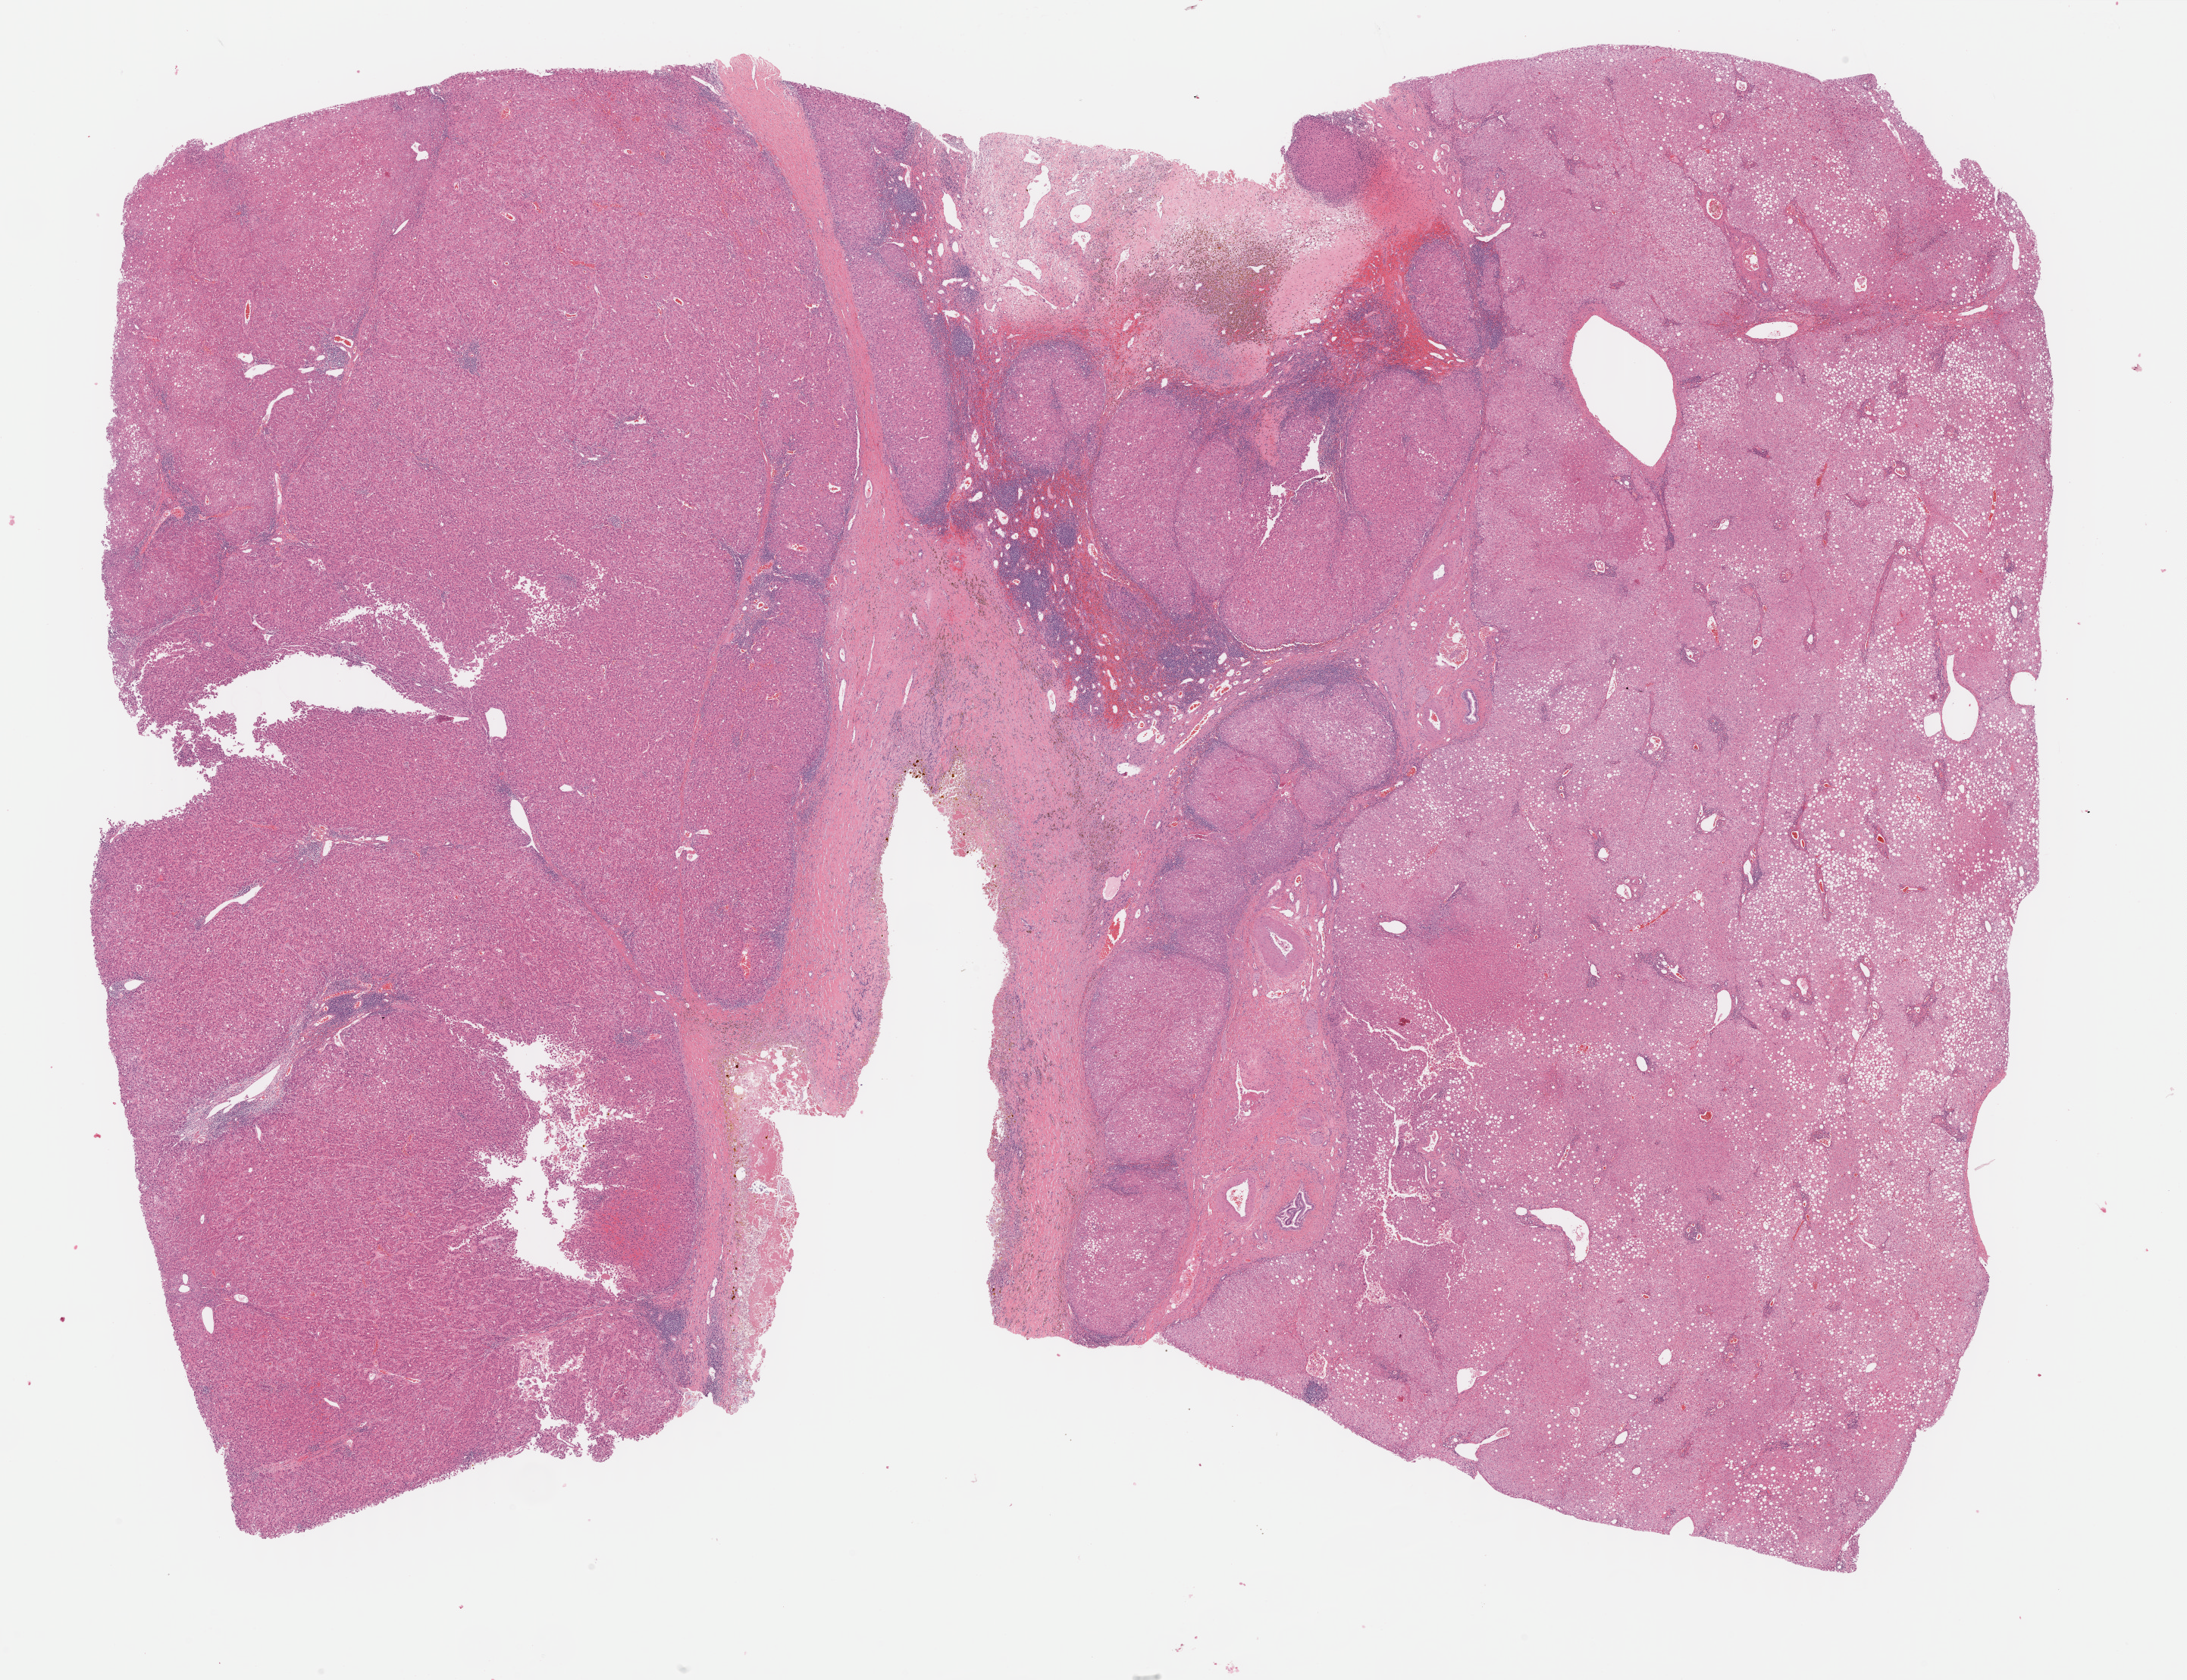
Whole-slide histology image, H&E, whole scanned area (about 23.4 x 17.9 mm) shown as a low-resolution overview; formalin-fixed paraffin-embedded (FFPE) diagnostic section; primary tumour sample from the liver. Male, age 67 years at initial diagnosis.
Diagnosis: Hepatocellular carcinoma, NOS.